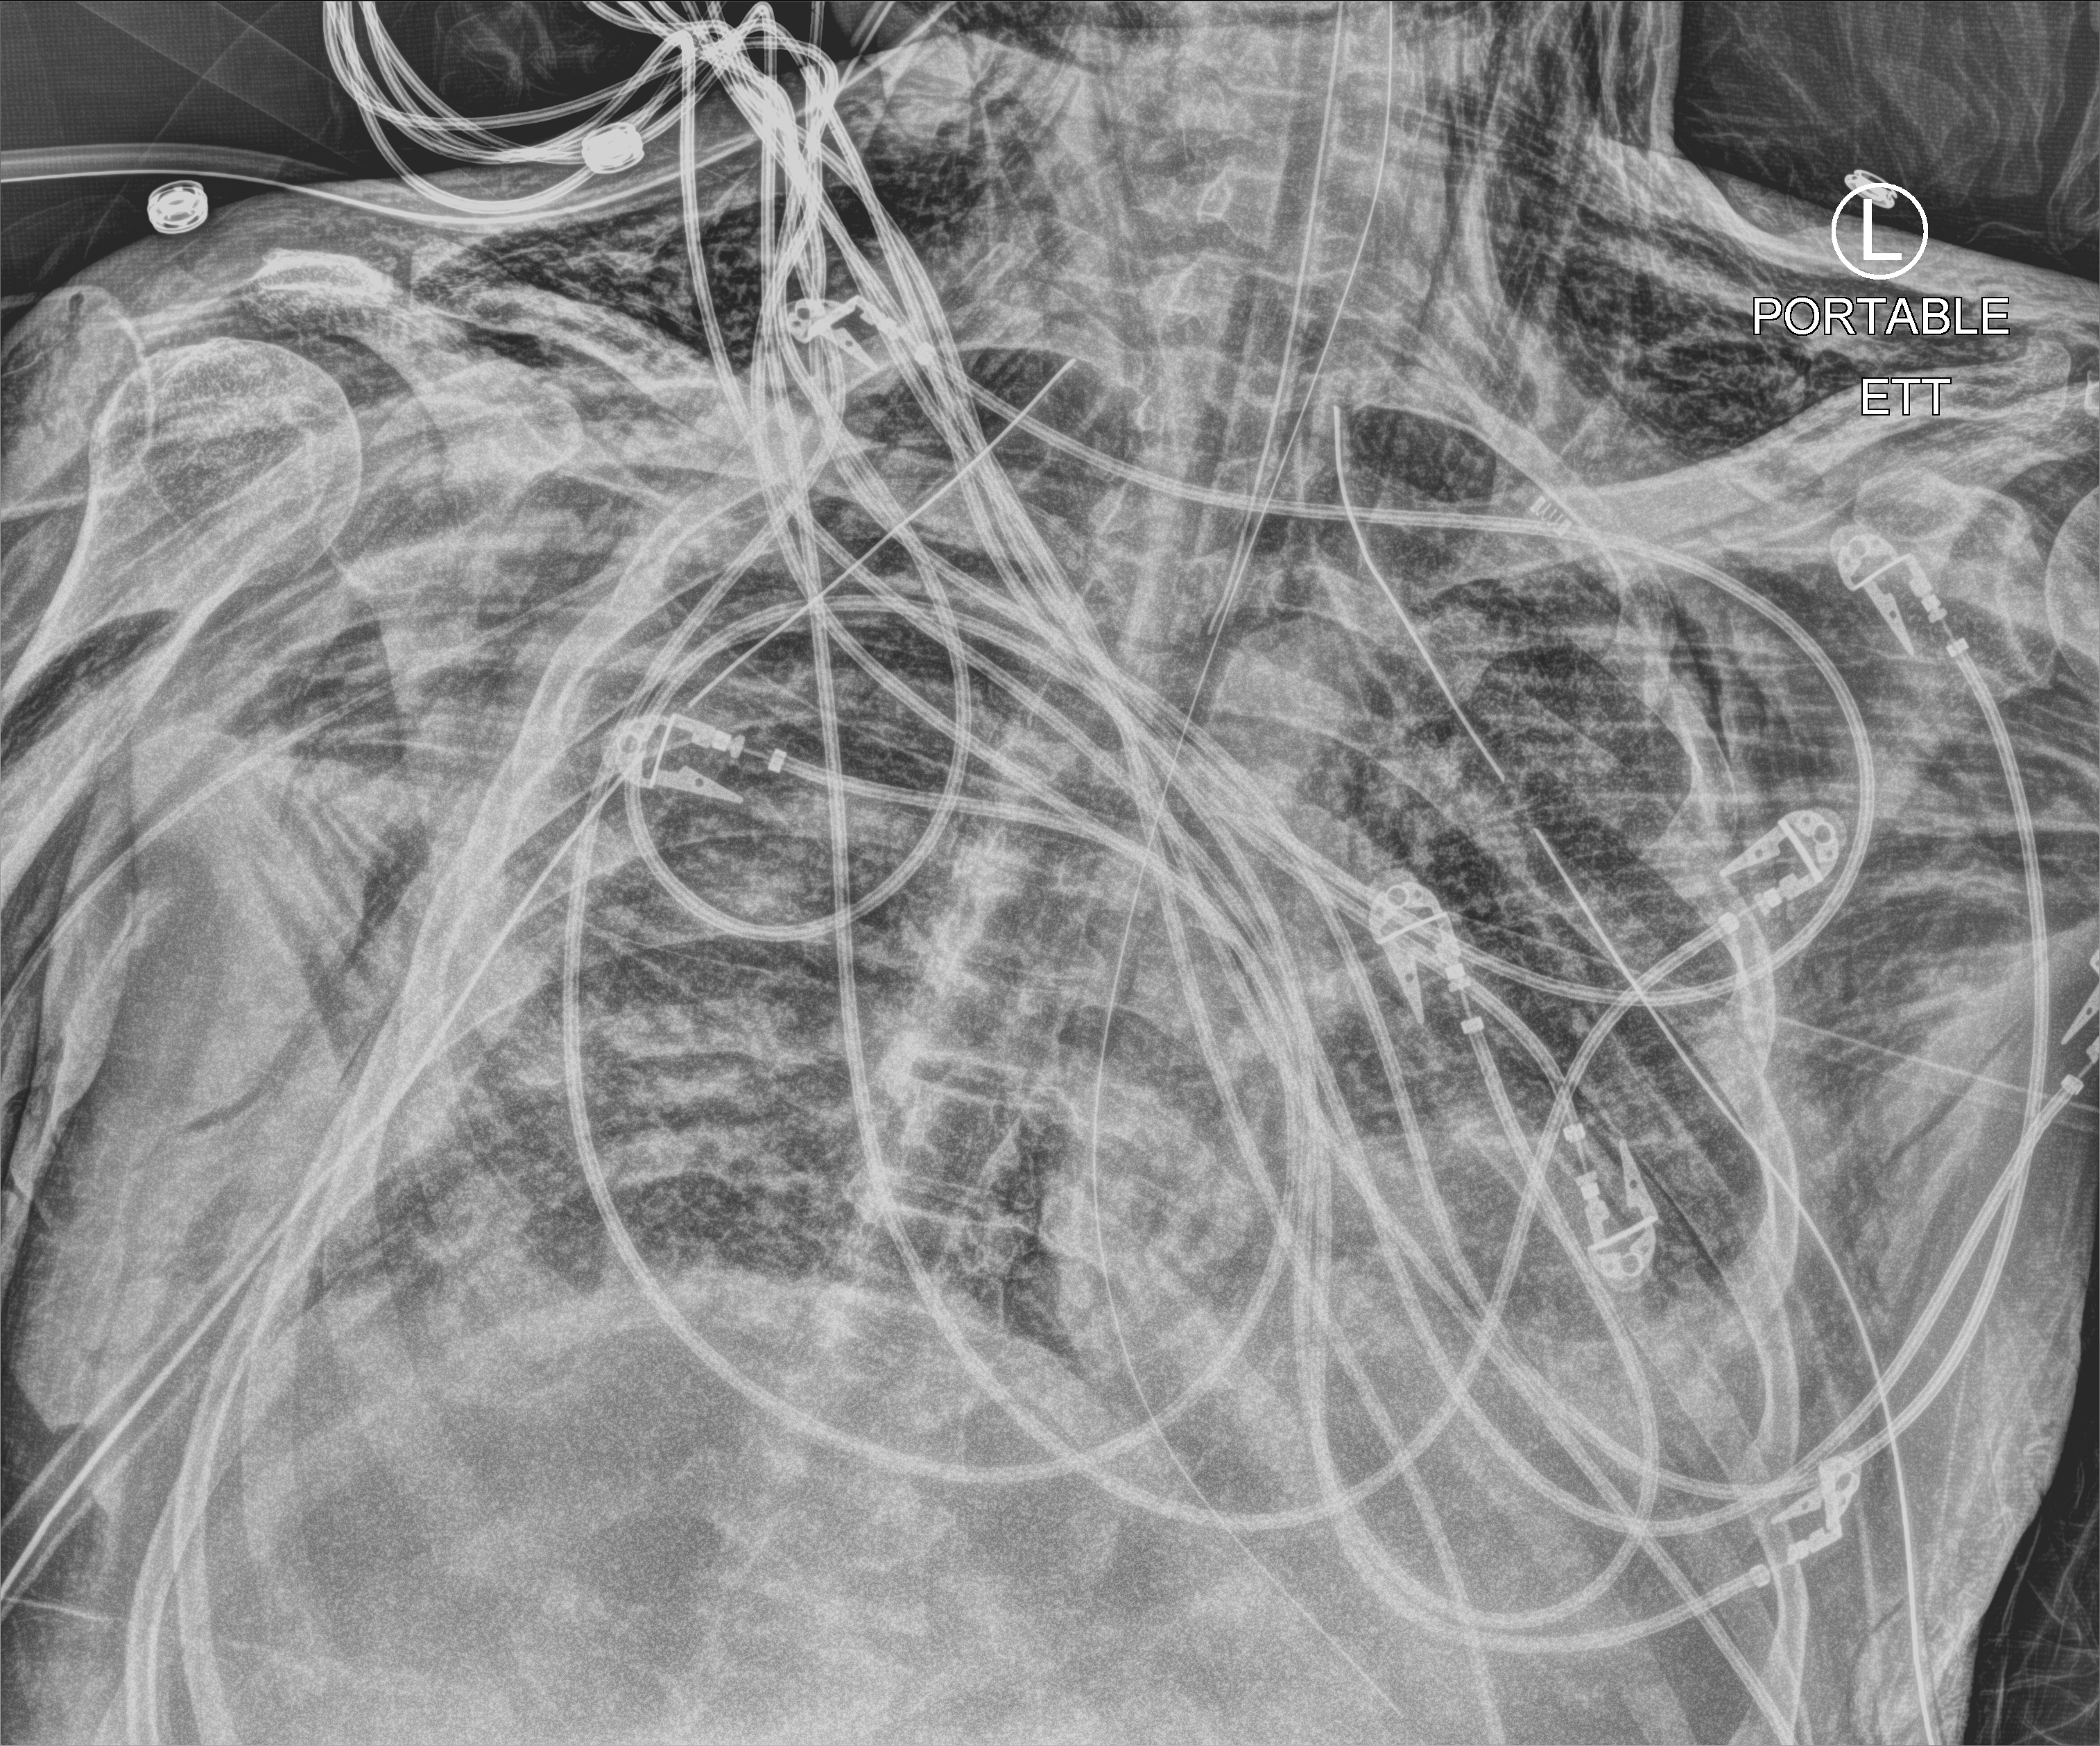
Chest X-ray (portable), anteroposterior (AP) projection. Male patient hospitalised with COVID-19, age 18–59 years.
From the hospital-stay record, not from the radiograph (when in the stay this image was taken is not recorded):
- chronic kidney disease (admission record): no
- admitted to intensive care during this hospital stay: yes